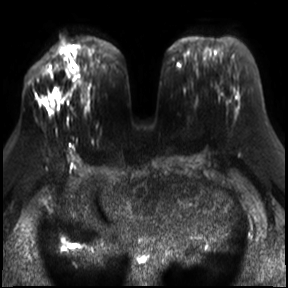
Breast MRI, one axial slice. Slice 14 of 30 in the series (ordered by position). Diffusion-weighted series; image 2 of 4 stored at this slice position (different b-values; order by instance number). 3 T. 4 mm slice thickness. 288 × 288 image matrix, field of view 340 × 340 mm. Female patient.
Structures marked on this image (manually delineated by an expert):
- tumour on diffusion-weighted imaging: bounding box <51,93,55,97> (left, top, right, bottom; pixels)